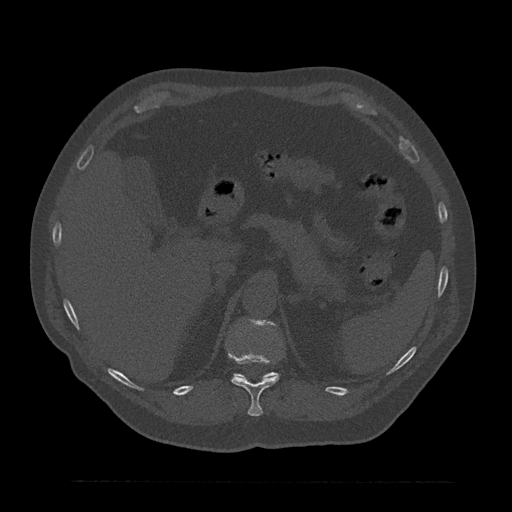
CT including the spine, one axial slice. Bone window (W 1800 / L 400 HU). 512 × 512 image matrix, field of view 430 × 430 mm. Male patient, age 61 years. Case-level facts recorded for this patient, not image findings: primary cancer: prostate.
Annotated regions visible in this slice (semi-automatic segmentation, software-assisted and operator-edited):
- T11 vertebra: bounding box [x1, y1, x2, y2] px = [227, 346, 279, 417]
- T12 vertebra: [235, 320, 278, 378]